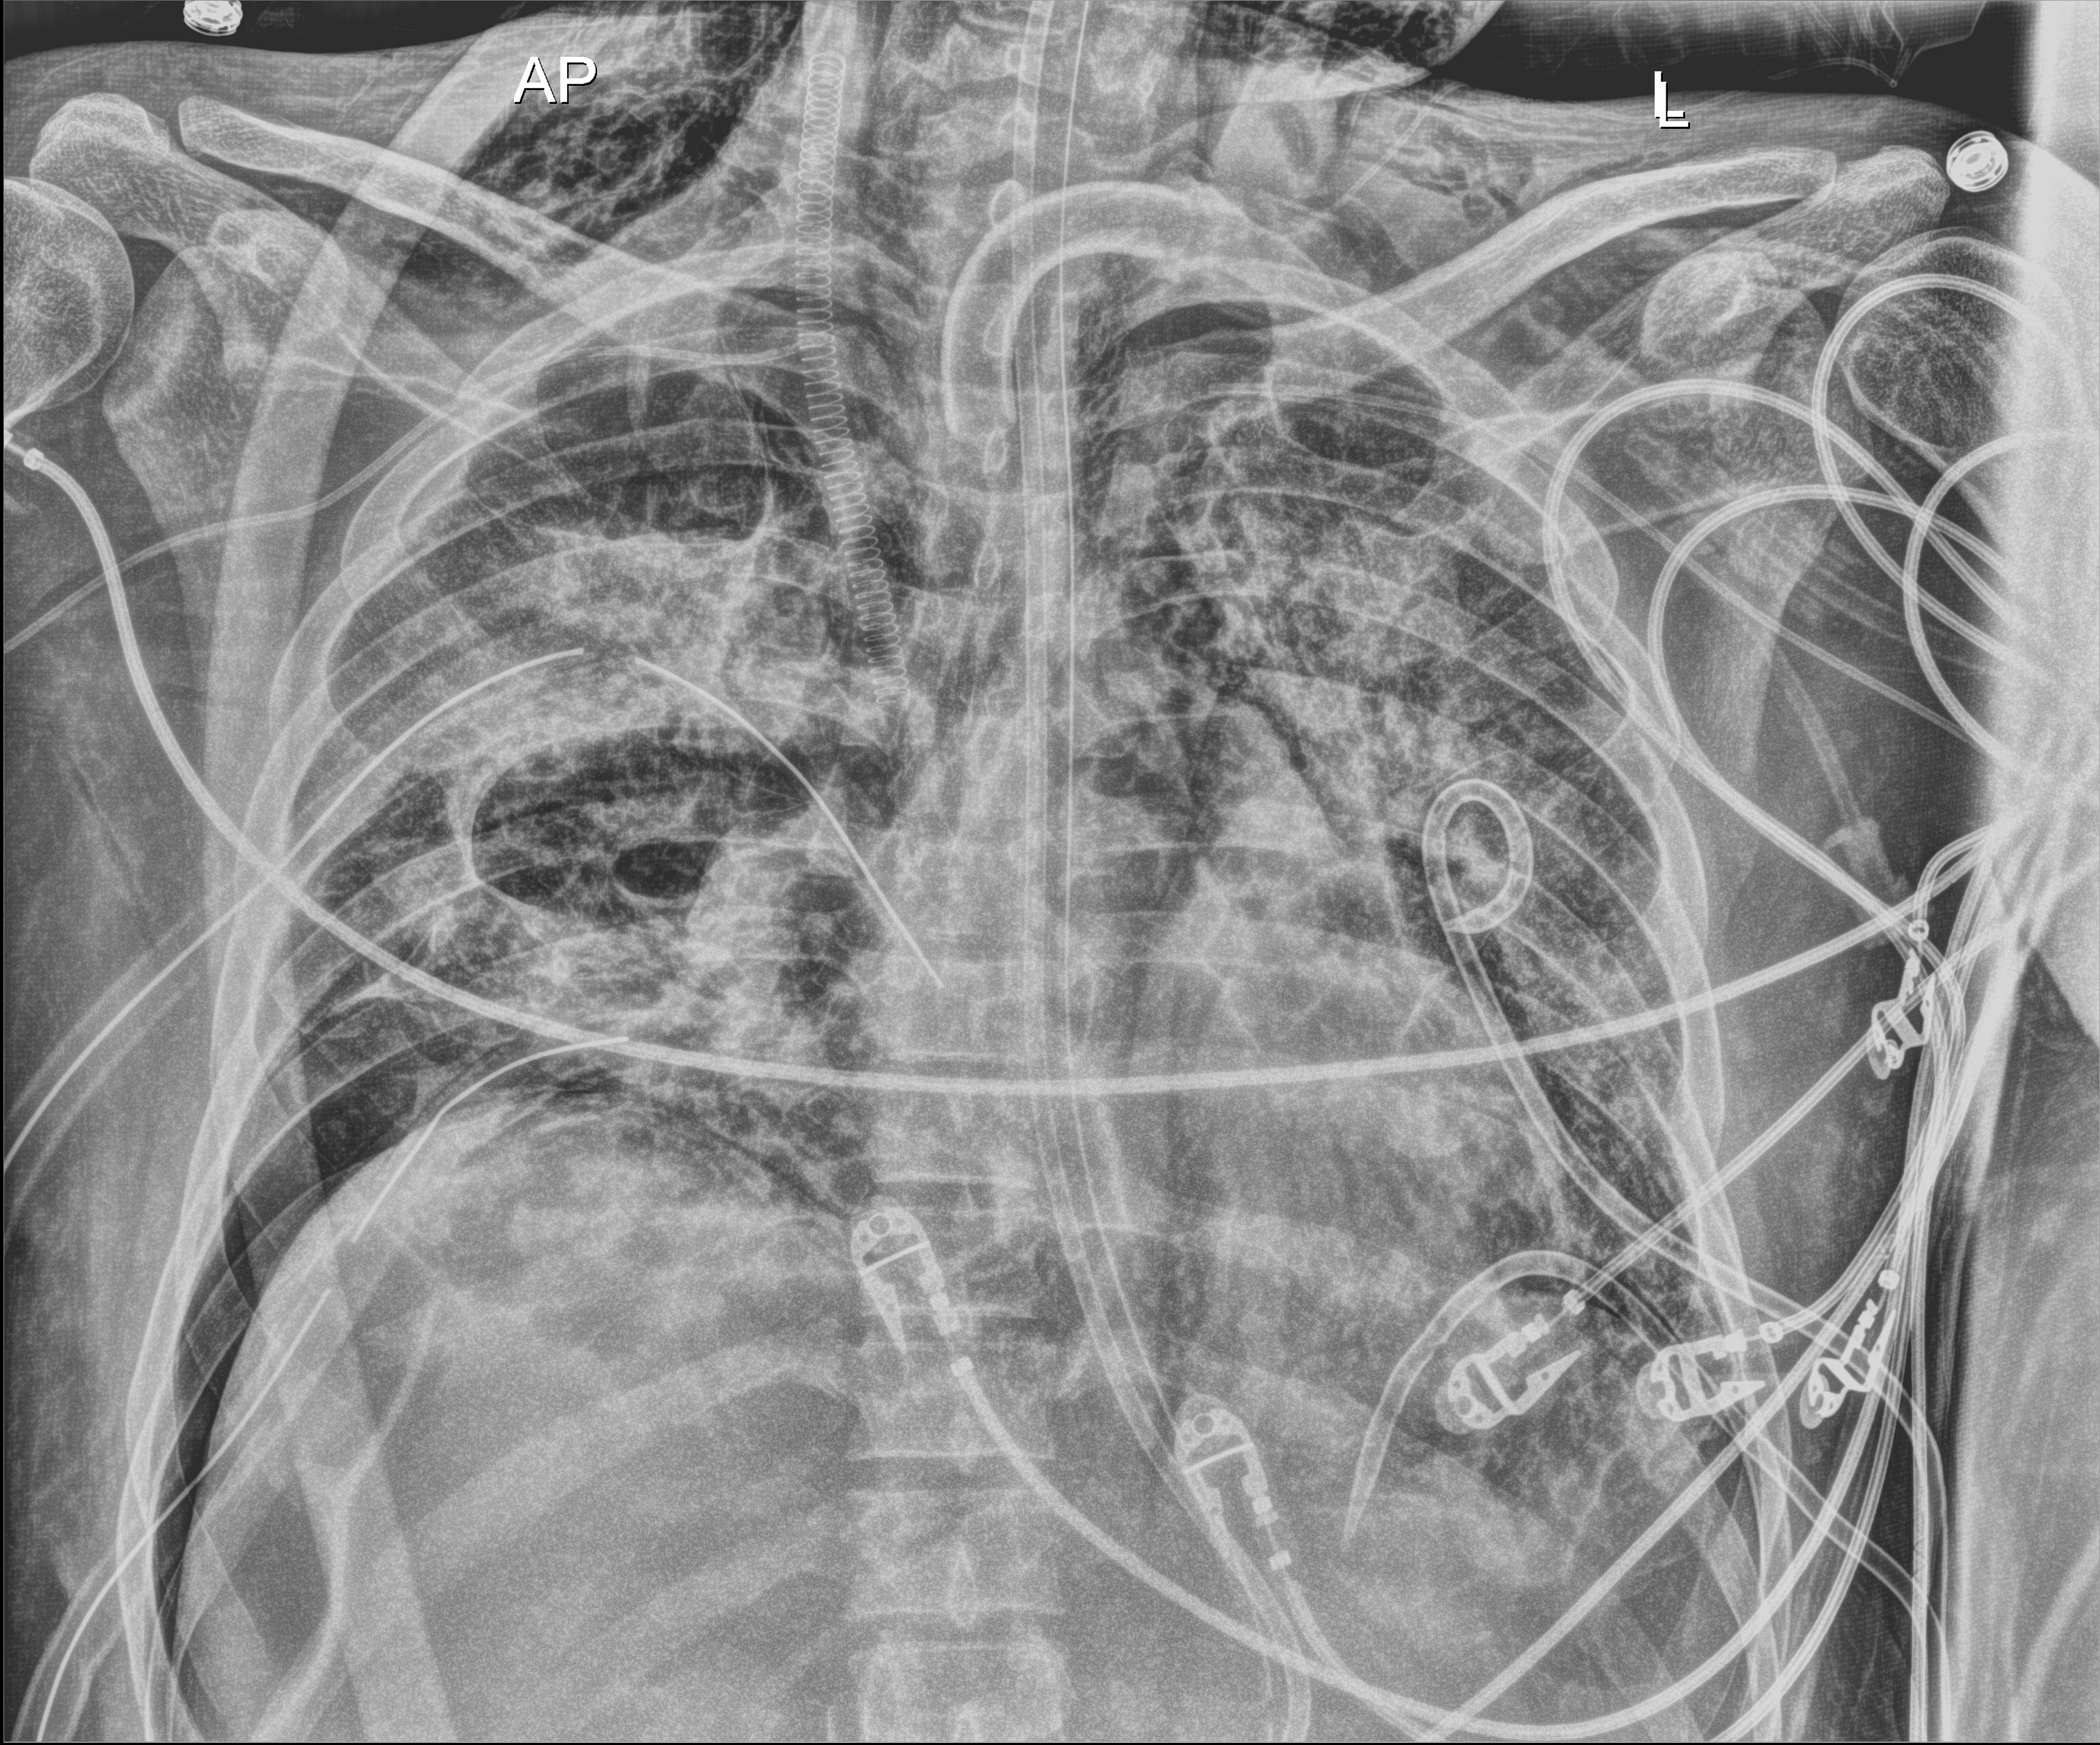
Bedside chest radiograph (digital radiography). Adult patient hospitalised with COVID-19, age 18–59 years.
From the hospital-stay record, not from the radiograph (when in the stay this image was taken is not recorded):
- mechanically ventilated during this hospital stay: yes
- diabetes (admission record): no
- admitted to intensive care during this hospital stay: yes